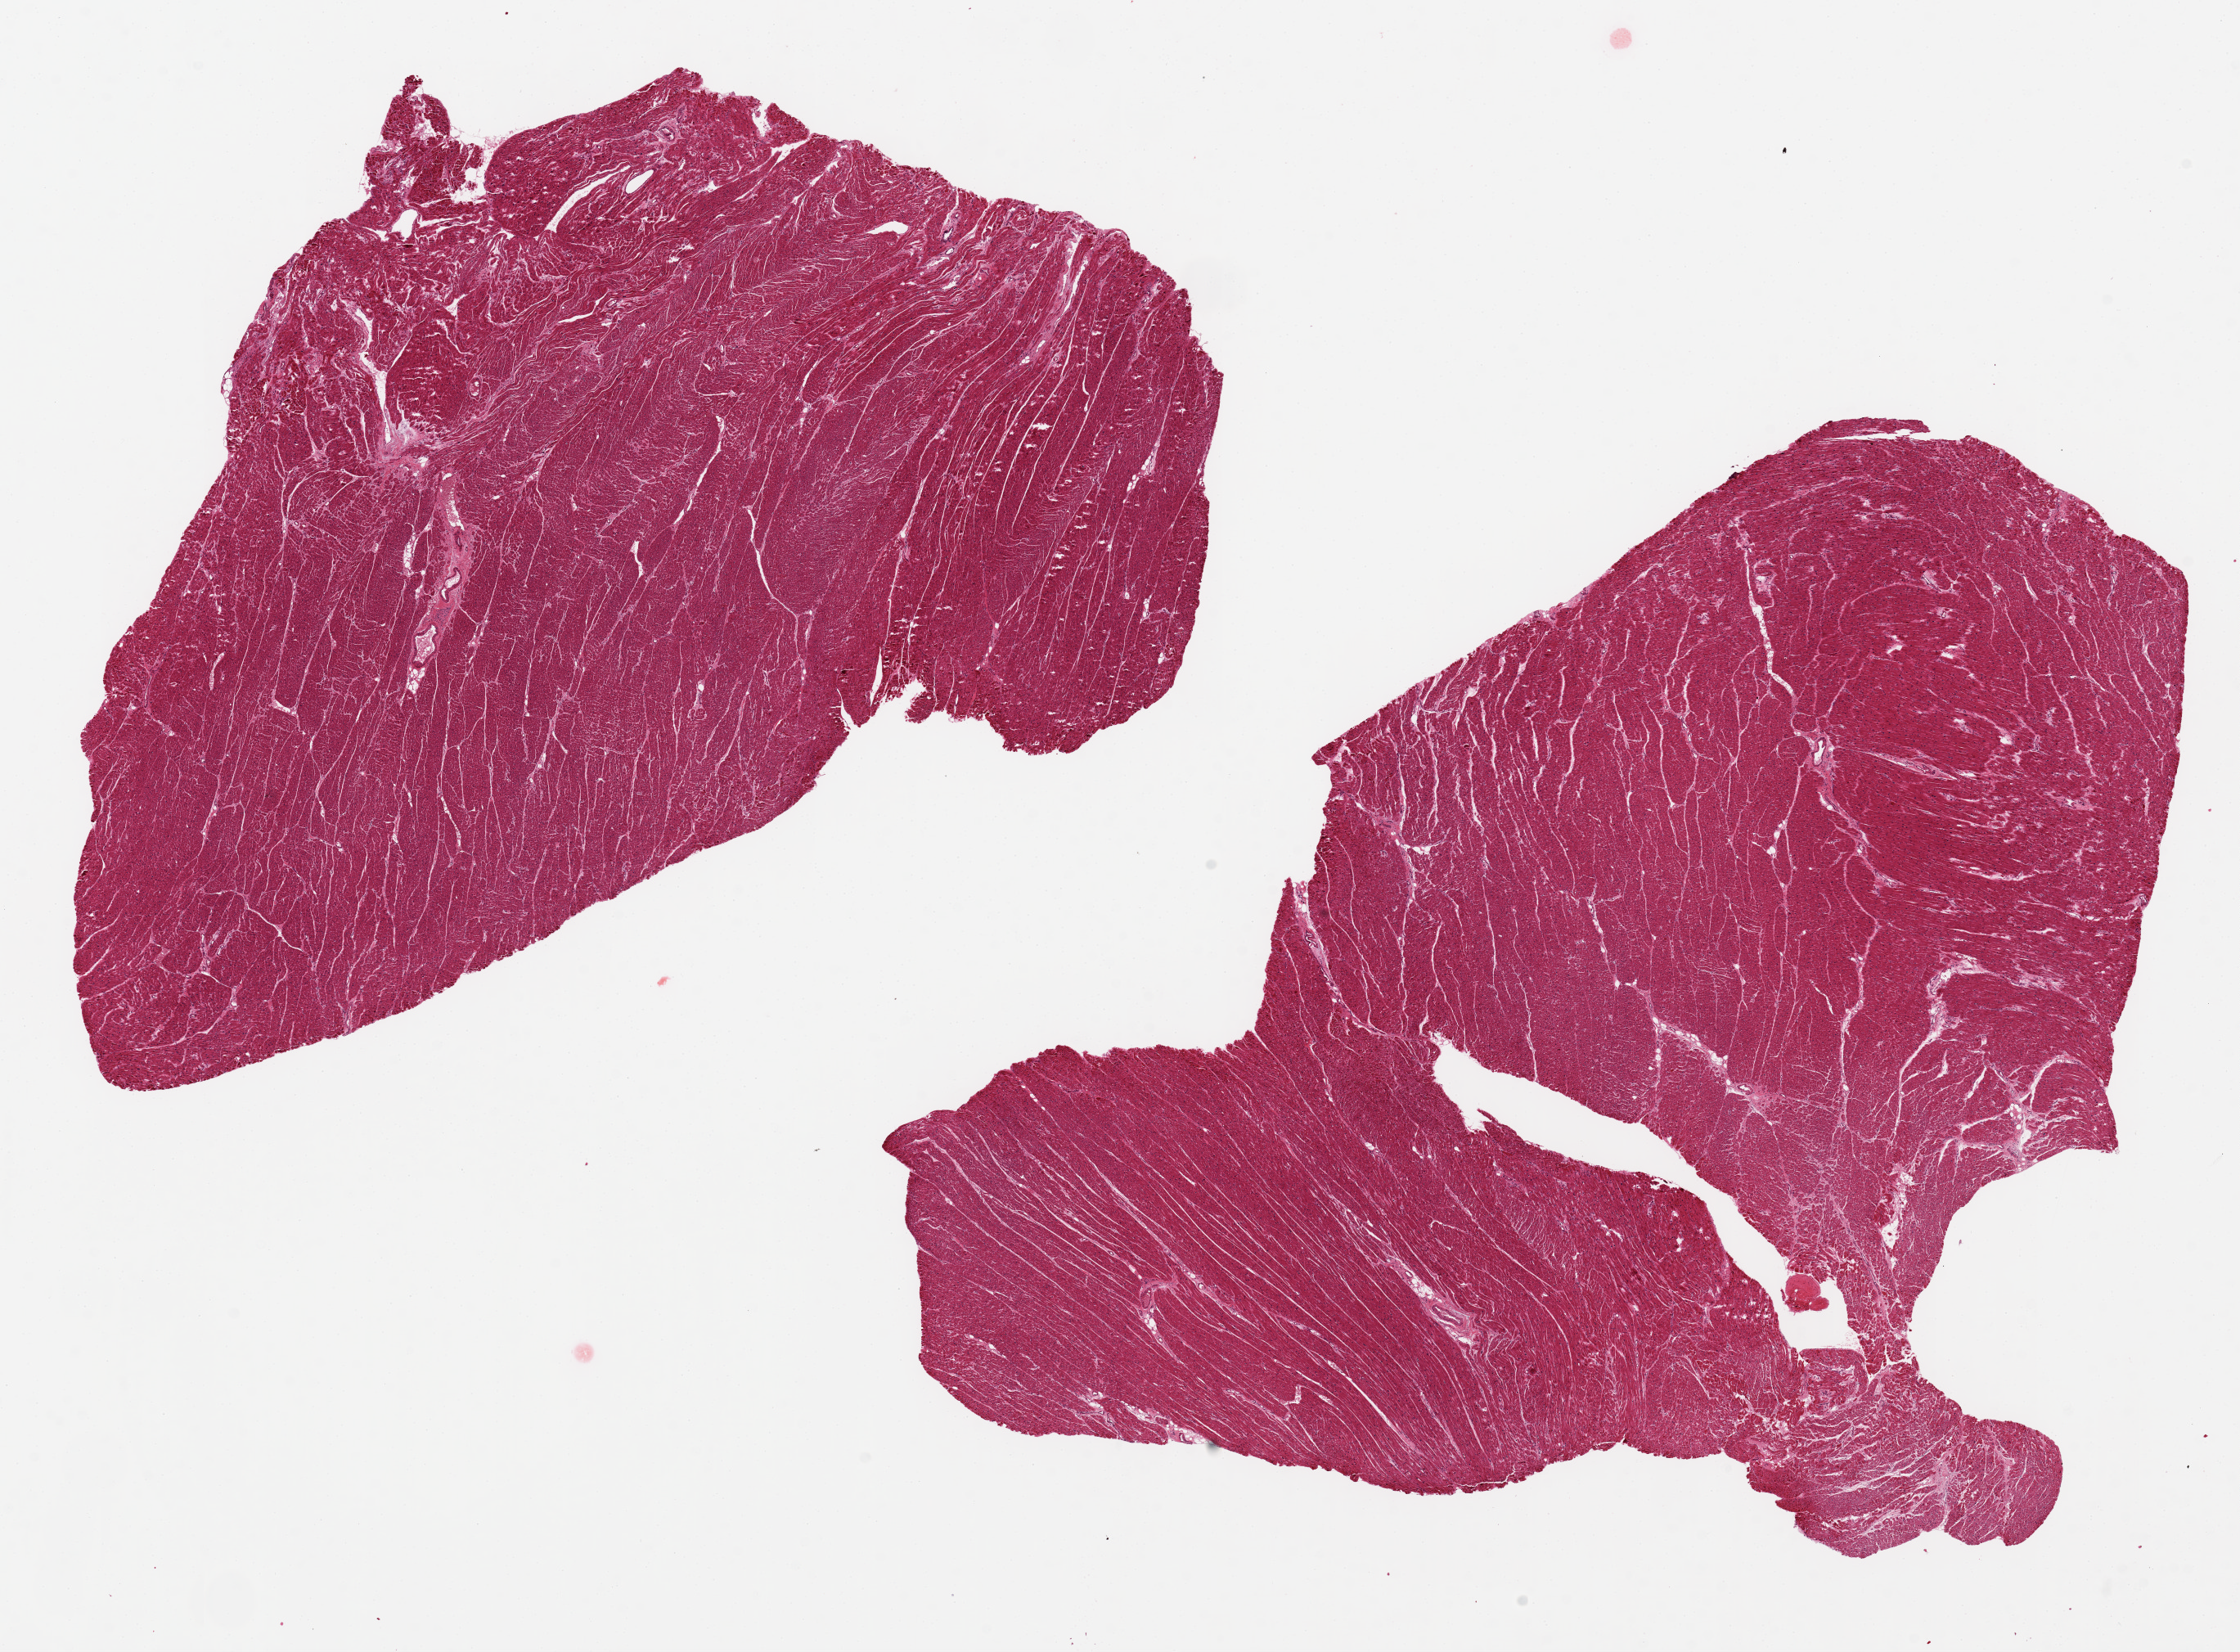
Digitized hematoxylin and eosin (H&E)-stained section — whole scanned area (about 21.7 x 16.0 mm, from a 20x scan) shown as a low-resolution overview, PAXgene-fixed, paraffin-embedded tissue, target tissue: heart, donor tissue sample. Donor: male.
Review note (as recorded): 2 ~11x10mm aliquots. Mild interstitial fibrosis, subacute ischemic changes (boxcar nuclei; contraction bands).